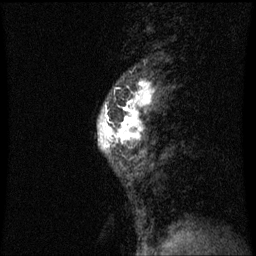
Breast MRI (dynamic contrast-enhanced), one sagittal slice. Position 21 of 60 along the scan axis. Dynamic contrast-enhanced series, image 2 of 3 at this slice position (ordered by acquisition). 1.5 T. TE 4.2 ms, TR 8.9 ms. 2 mm slice thickness. 256 × 256 image matrix, field of view 200 × 200 mm. Patient: female, 50 years. Case-level facts recorded for this patient, not image findings: setting: breast cancer imaged before/during neoadjuvant chemotherapy; receptor status: triple-negative.
Annotated regions visible in this slice (semi-automatically segmented with operator editing):
- analysis volume of interest (the breast-tissue region the enhancement analysis was run in; not a lesion): bounding box <98,80,163,171> (left, top, right, bottom; pixels)
- tumour enhancement mask (voxels above the 70 % enhancement threshold inside the analysis volume of interest): <104,80,151,149>